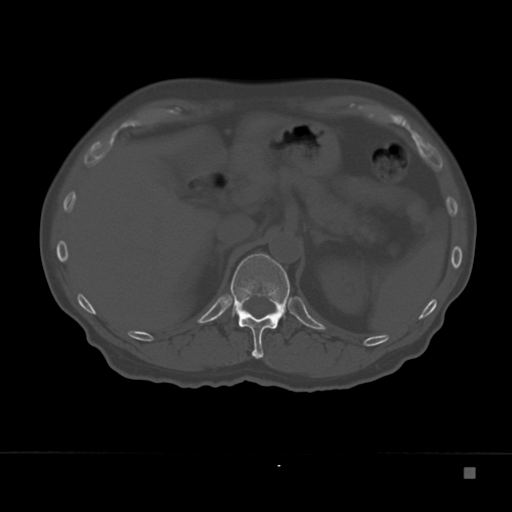
CT including the spine, one axial slice; position 130 of 332 along the scan axis; 120 kVp; bone window (W 1800 / L 400 HU); 512 × 512 image matrix, field of view 389 × 389 mm. Patient: male, 72 years. Case-level facts recorded for this patient, not image findings: primary cancer: skeletal.
Structures marked on this image (semi-automatically segmented with operator editing):
- T12 vertebra: bounding box (x1, y1, x2, y2) in pixels: (230, 253, 290, 359)